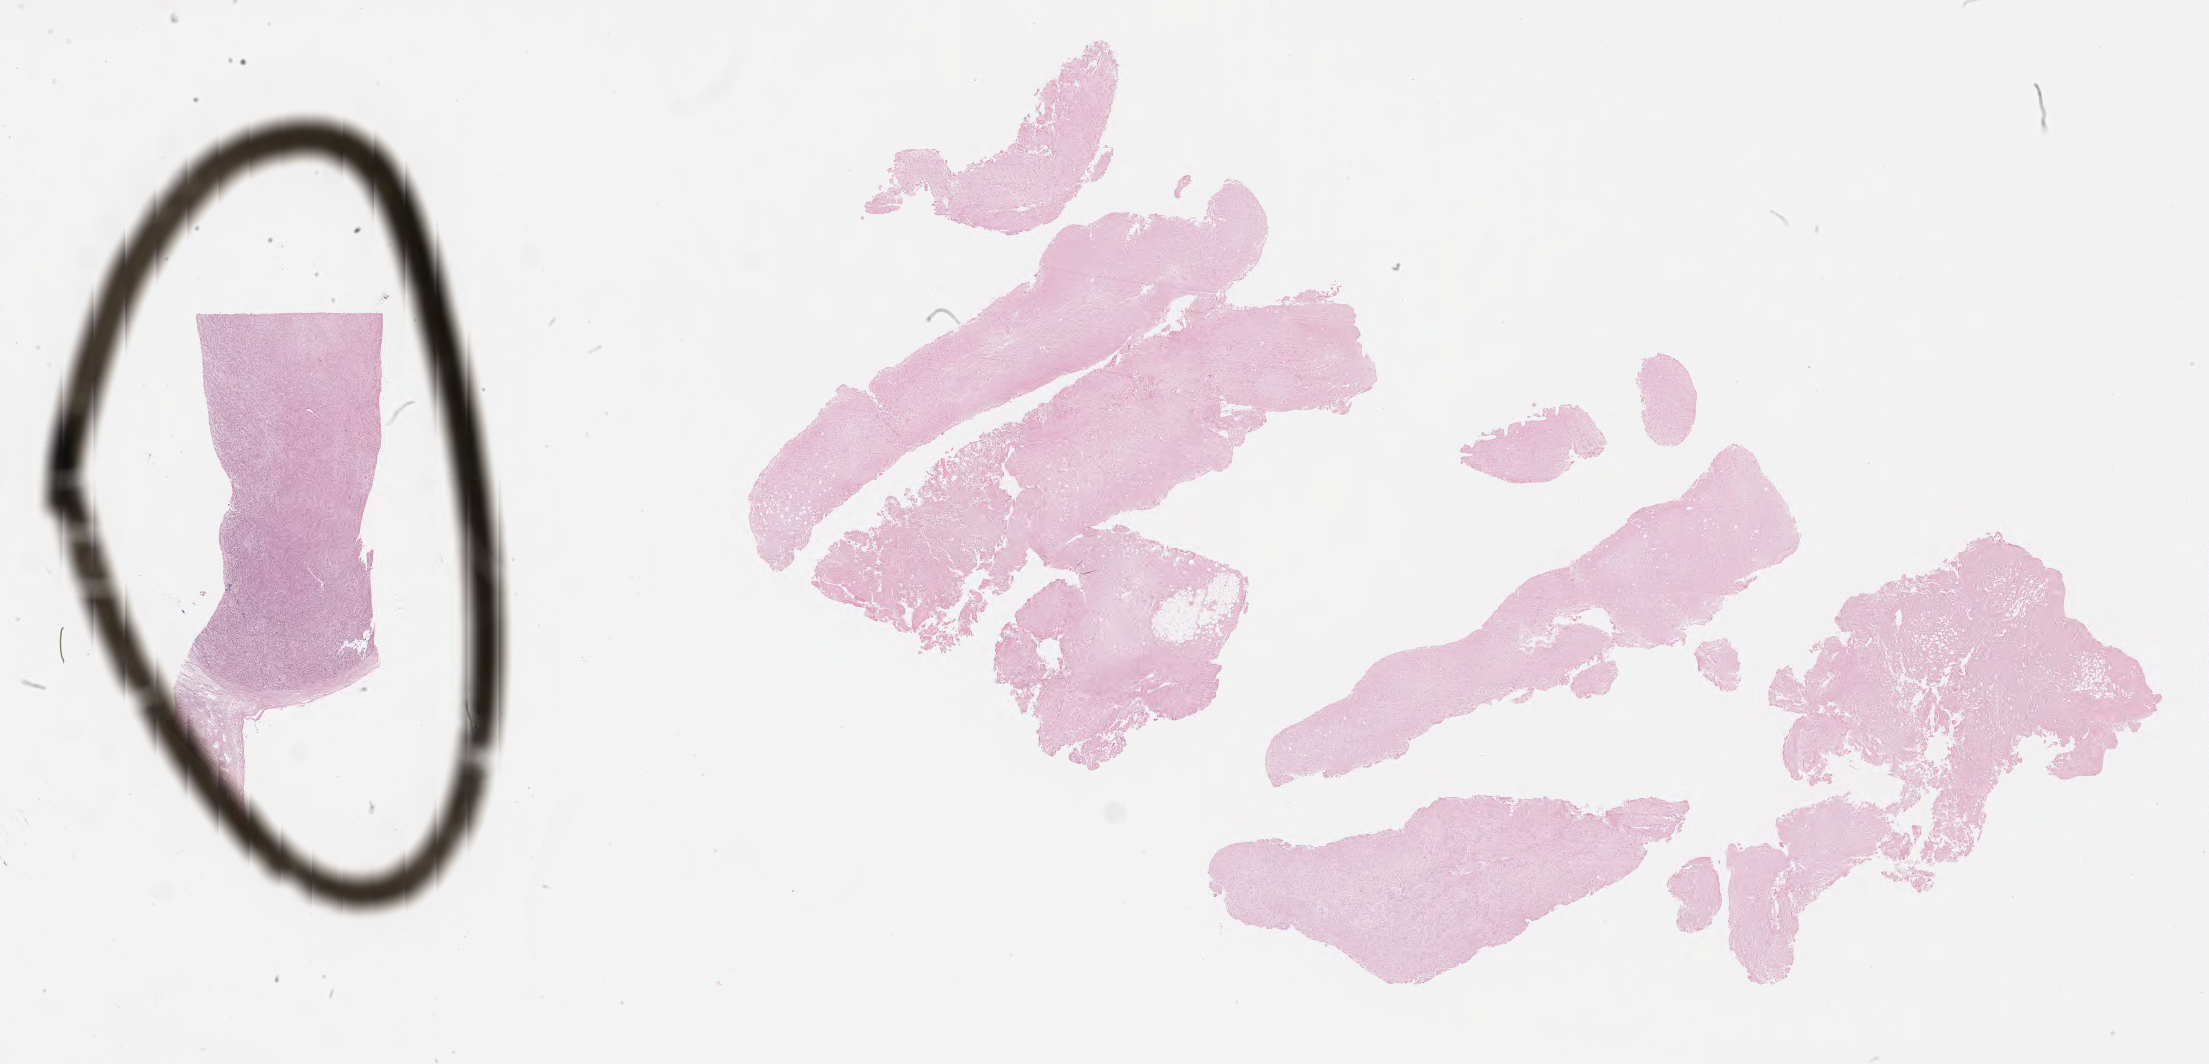
Whole-slide image; stain recorded as Iodonitrotetrazolium, whole scanned area (about 35.7 x 17.2 mm) shown as a low-resolution overview; specimen: tumor tissue. Male patient, aged 45.
Histologic diagnosis: Diffuse large B-cell lymphoma, NOS.